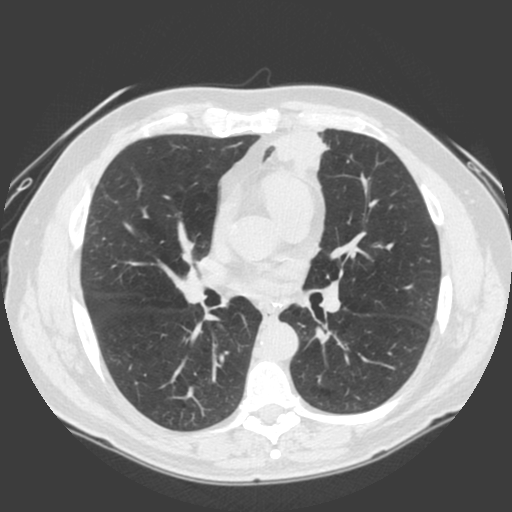
Low-dose screening chest CT, one axial slice; slice 99 of 185 in the series (ordered by position); lung window (W 1500 / L -600 HU); 512 × 512 image matrix, field of view 360 × 360 mm.
Outlined on this slice (expert manual segmentation):
- lesion 1 (tumor, lower lobe of left lung): box from (x=275, y=132) to (x=330, y=170) px